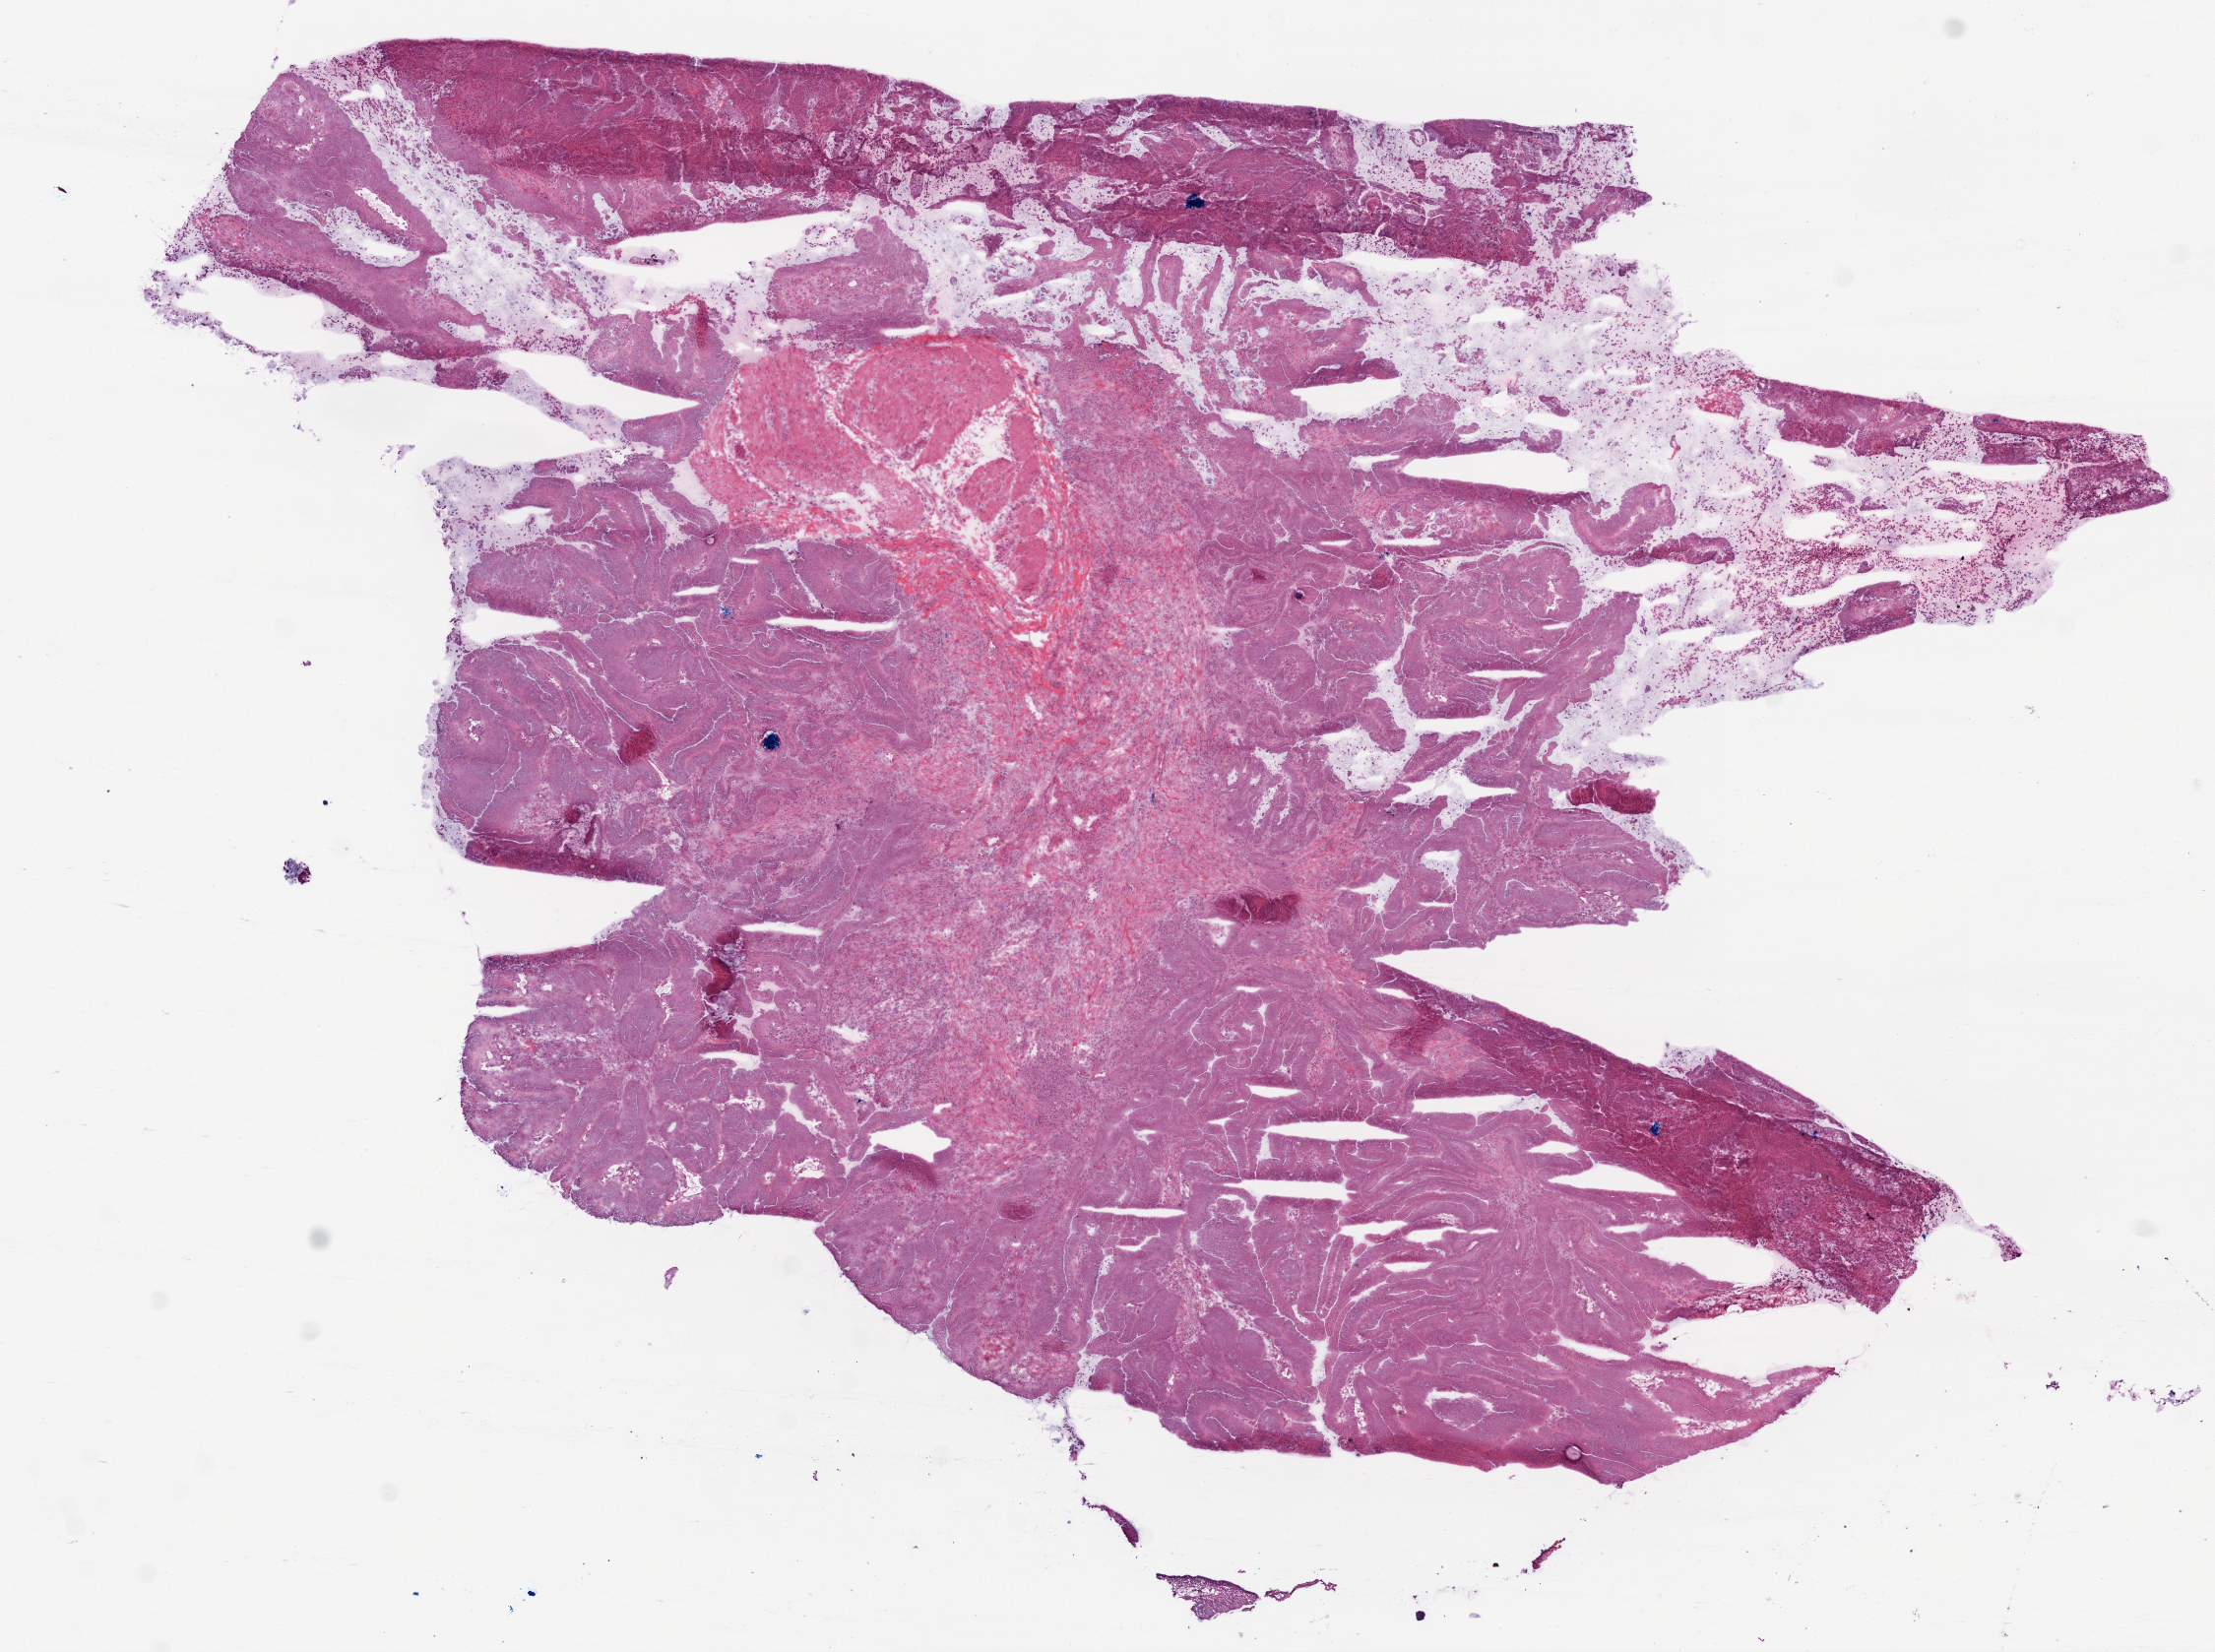
Whole-slide histology image, H&E, low-resolution overview of the scanned area, about 9.0 x 6.7 mm; frozen section from the bottom of the tissue portion; primary tumour sample from the colon. Patient: female, age at initial diagnosis 83 years. Composition of this section per pathologist review: tumour cells 77%, tumour nuclei 85%, normal cells 8%, stromal cells 10%, necrosis 5%.
AJCC pathologic stage: I (6th edition). Lymph nodes positive (case pathology): 0 of 18 examined. TNM: T1 N0 M0. Histologic diagnosis: Mucinous adenocarcinoma (transverse colon).